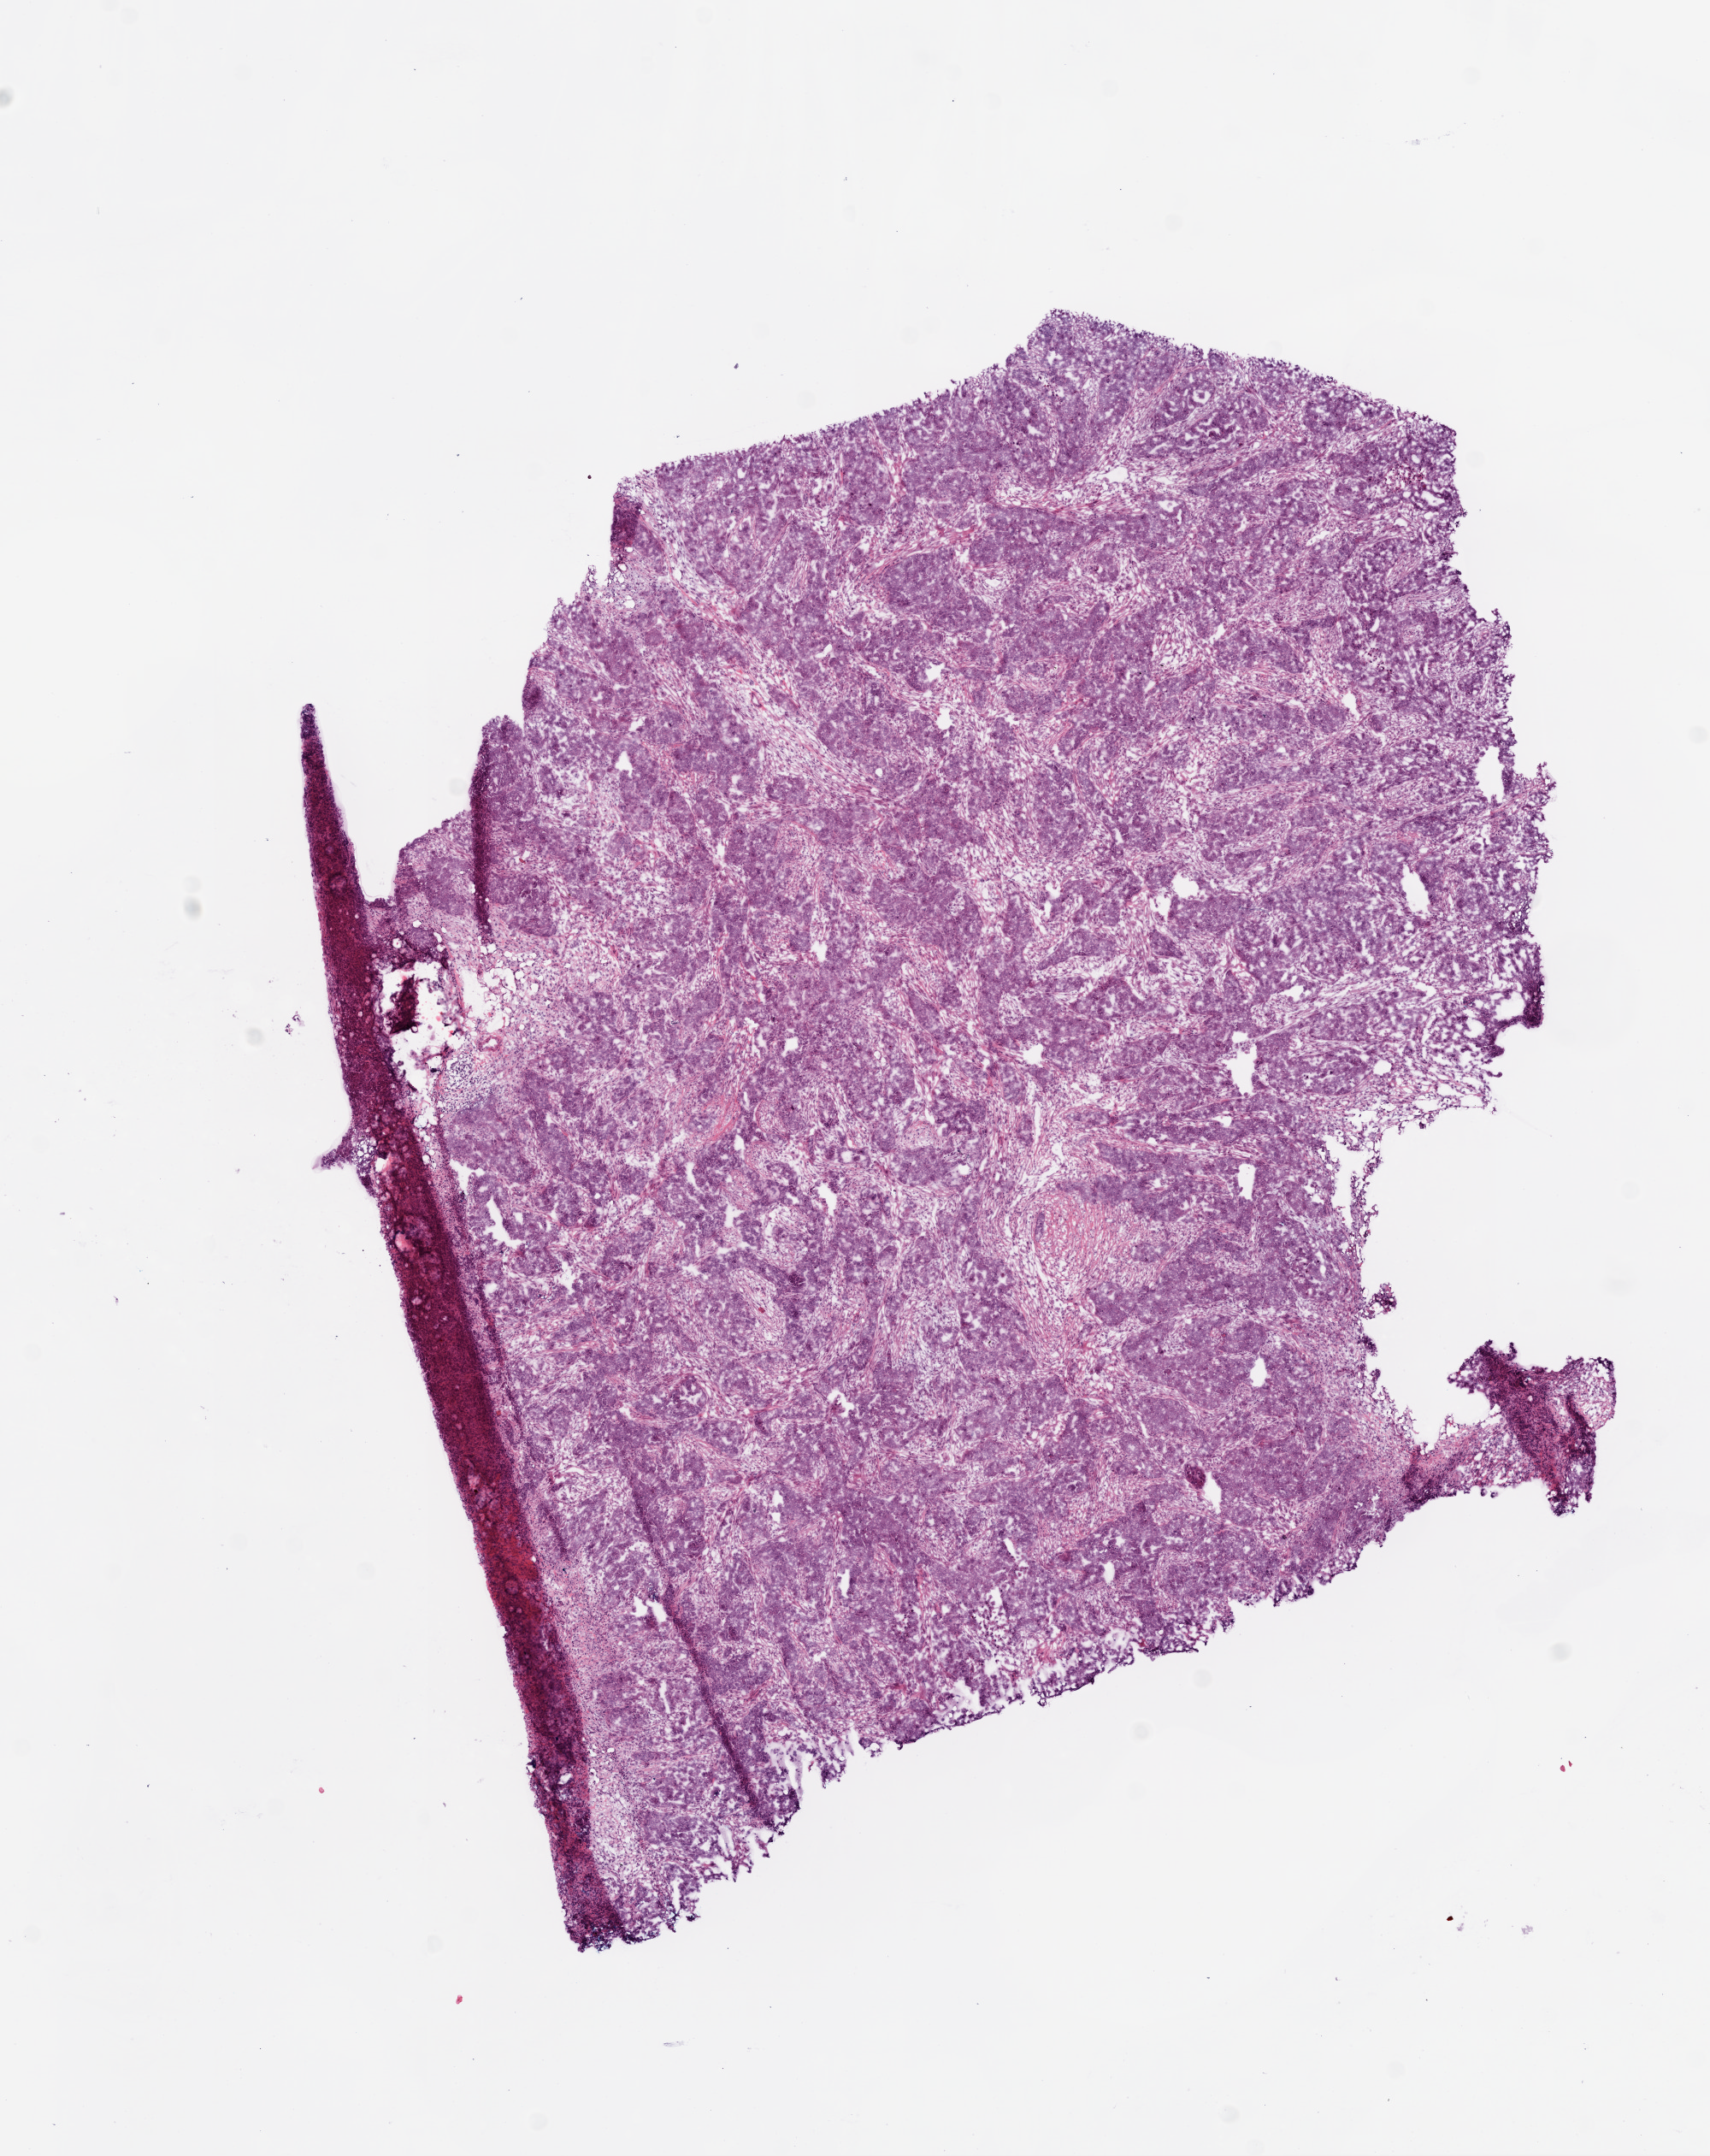
H&E-stained whole-slide image — low-resolution overview of the scanned area, about 8.0 x 10.1 mm, frozen section from the bottom of the tissue portion, sample: primary tumour, ovary. Female patient; age at initial diagnosis 49 years. Histologic grade: G3 (poorly differentiated). Composition of this section per pathologist review: tumour cells 70%, tumour nuclei 80%, normal cells 0%, stromal cells 30%, necrosis 0%.
Diagnosis: Serous cystadenocarcinoma, NOS. FIGO stage: IIIC. Laterality: bilateral.